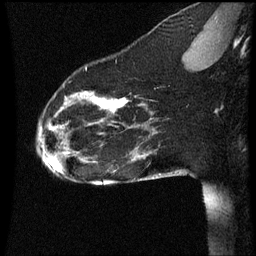
Breast MRI (dynamic contrast-enhanced), one sagittal slice. Position 17 of 60 along the scan axis. Dynamic contrast-enhanced series, image 2 of 3 at this slice position (ordered by acquisition). 1.5 T. TE 4.2 ms, TR 8.9 ms. 2 mm slice thickness. 256 × 256 image matrix, field of view 200 × 200 mm. Female patient, age 35 years. Case-level facts recorded for this patient, not image findings: setting: breast cancer imaged before/during neoadjuvant chemotherapy; receptor status: HER2-positive.
Annotated regions visible in this slice (semi-automatic segmentation, software-assisted and operator-edited):
- analysis volume of interest (the breast-tissue region the enhancement analysis was run in; not a lesion): box from (x=35, y=66) to (x=177, y=177) px
- tumour enhancement mask (voxels above the 70 % enhancement threshold inside the analysis volume of interest): (x=66, y=98)–(x=129, y=125)